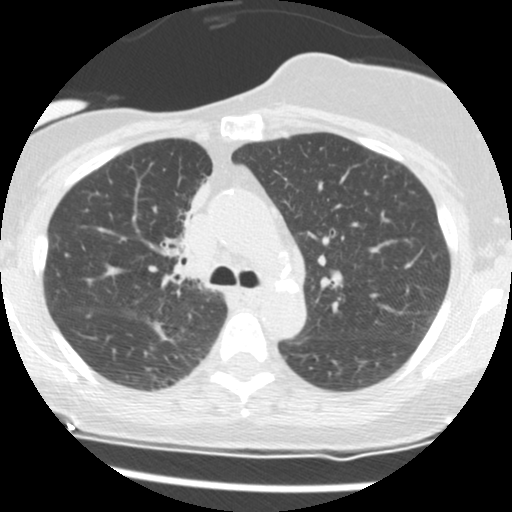
Chest CT (low-dose screening protocol), one axial image; second annual screen; lung window (W 1500 / L -600 HU); slice 45 of 165 in the series. Female, age 56 years at enrolment. Current smoker at enrolment.
- Expert reader's lesion annotation, bounding box <153,183,210,268> (left, top, right, bottom; pixels).
- The screening reader recorded 2 non-calcified nodules or masses ≥4 mm on this exam (right middle lobe, right lower lobe); which of them this box marks is not recorded.
- Participant outcome: lung cancer diagnosed 675 days after this screen (after the third annual screen) — adenocarcinoma, NOS, right upper lobe, stage IIIB (AJCC 6th edition), 8 mm at pathology.